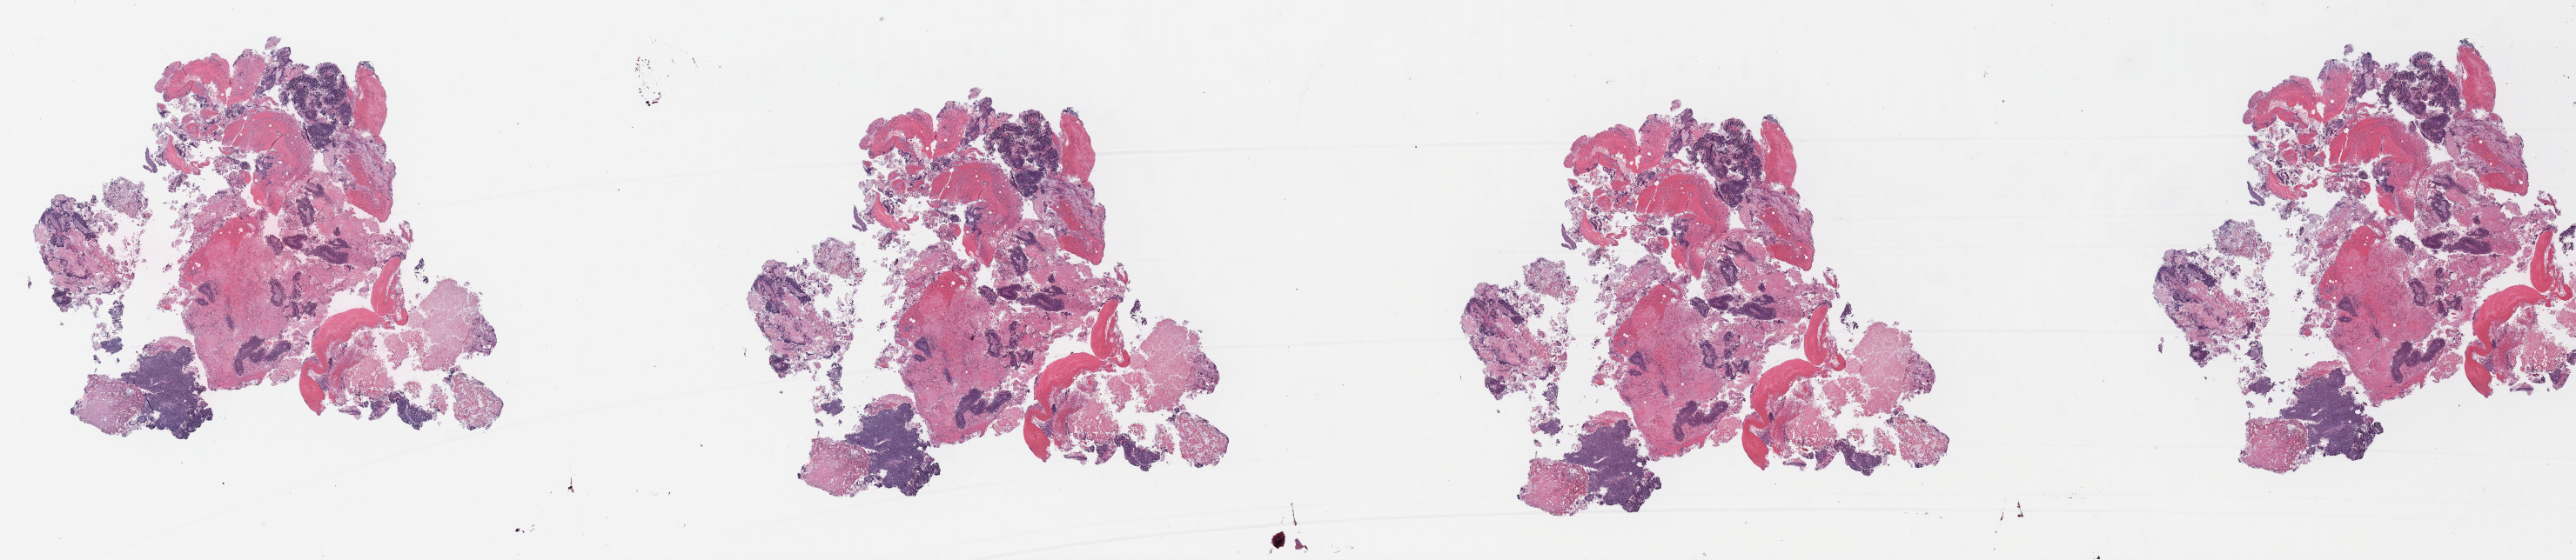
Whole-slide histology image, H&E — a low-resolution overview of the entire scanned area, about 46.5 x 10.1 mm (acquisition: 40x scan), FFPE section, sample: primary tumour, bladder. Patient: female, age at initial diagnosis 80 years. Histologic grade: high grade.
* diagnosis: Transitional cell carcinoma (posterior wall of bladder)
* AJCC pathologic stage: III (7th edition)